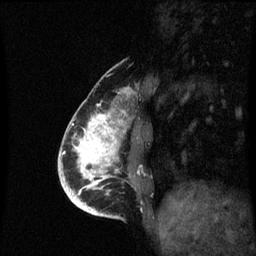
Breast MRI (dynamic contrast-enhanced), one sagittal slice. Position 20 of 60 along the scan axis. Dynamic contrast-enhanced series, image 2 of 3 at this slice position (ordered by acquisition). 1.5 T. TE 4.2 ms, TR 8.9 ms. 2 mm slice thickness. 256 × 256 image matrix, field of view 200 × 200 mm. Patient: female, 35 years. From the clinical record (not read from this slice): setting: breast cancer imaged before/during neoadjuvant chemotherapy; receptor status: HR-positive, HER2-negative.
Annotated regions visible in this slice (semi-automatic segmentation, software-assisted and operator-edited):
- analysis volume of interest (the breast-tissue region the enhancement analysis was run in; not a lesion): box from (x=66, y=102) to (x=132, y=215) px
- tumour enhancement mask (voxels above the 70 % enhancement threshold inside the analysis volume of interest): (x=69, y=114)–(x=118, y=215)